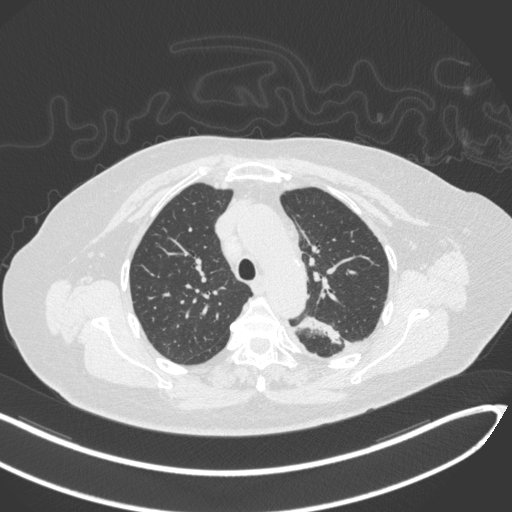
Chest CT, one axial slice. Position 231 of 270 along the scan axis. Reconstruction kernel B31f. Lung window (W 1500 / L -600 HU). 1 mm slice thickness. 512 × 512 image matrix, field of view 400 × 400 mm. Female patient, age 76 years. From the clinical record (not read from this slice): clinical TNM (as recorded): T1c N0 M0.
Structures marked on this image (rectangle marked by the reading radiologist):
- lung tumour (recorded histology: adenocarcinoma): box from (x=296, y=311) to (x=344, y=346) px